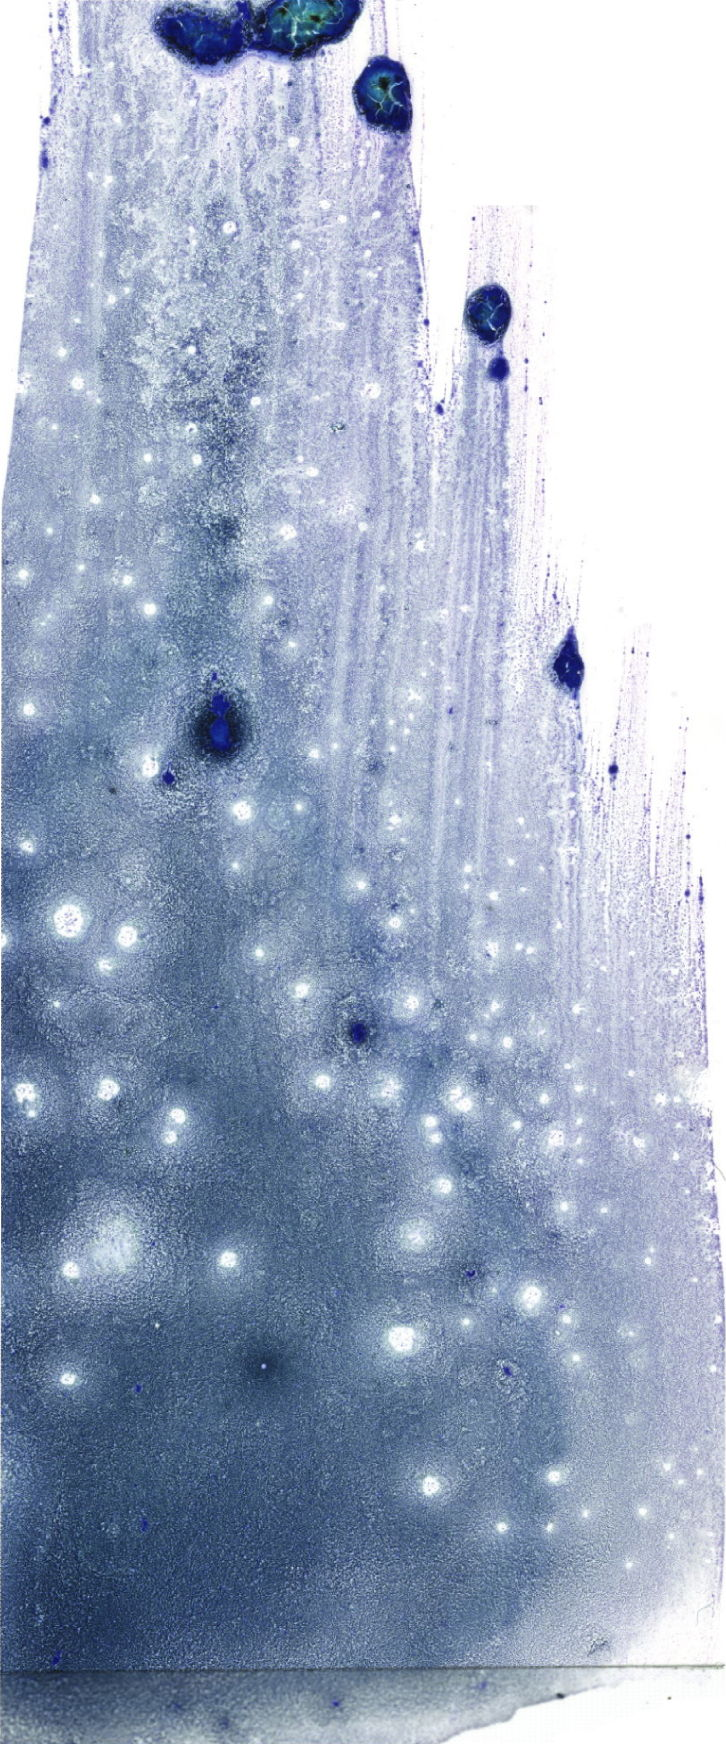
May-Grünwald-Giemsa (MGG)-stained marrow aspirate smear (whole slide), a low-resolution overview of the entire scanned area, about 20.6 x 49.4 mm. Patient sex: female.
• diagnosis: Acute Myeloid Leukemia with Maturation